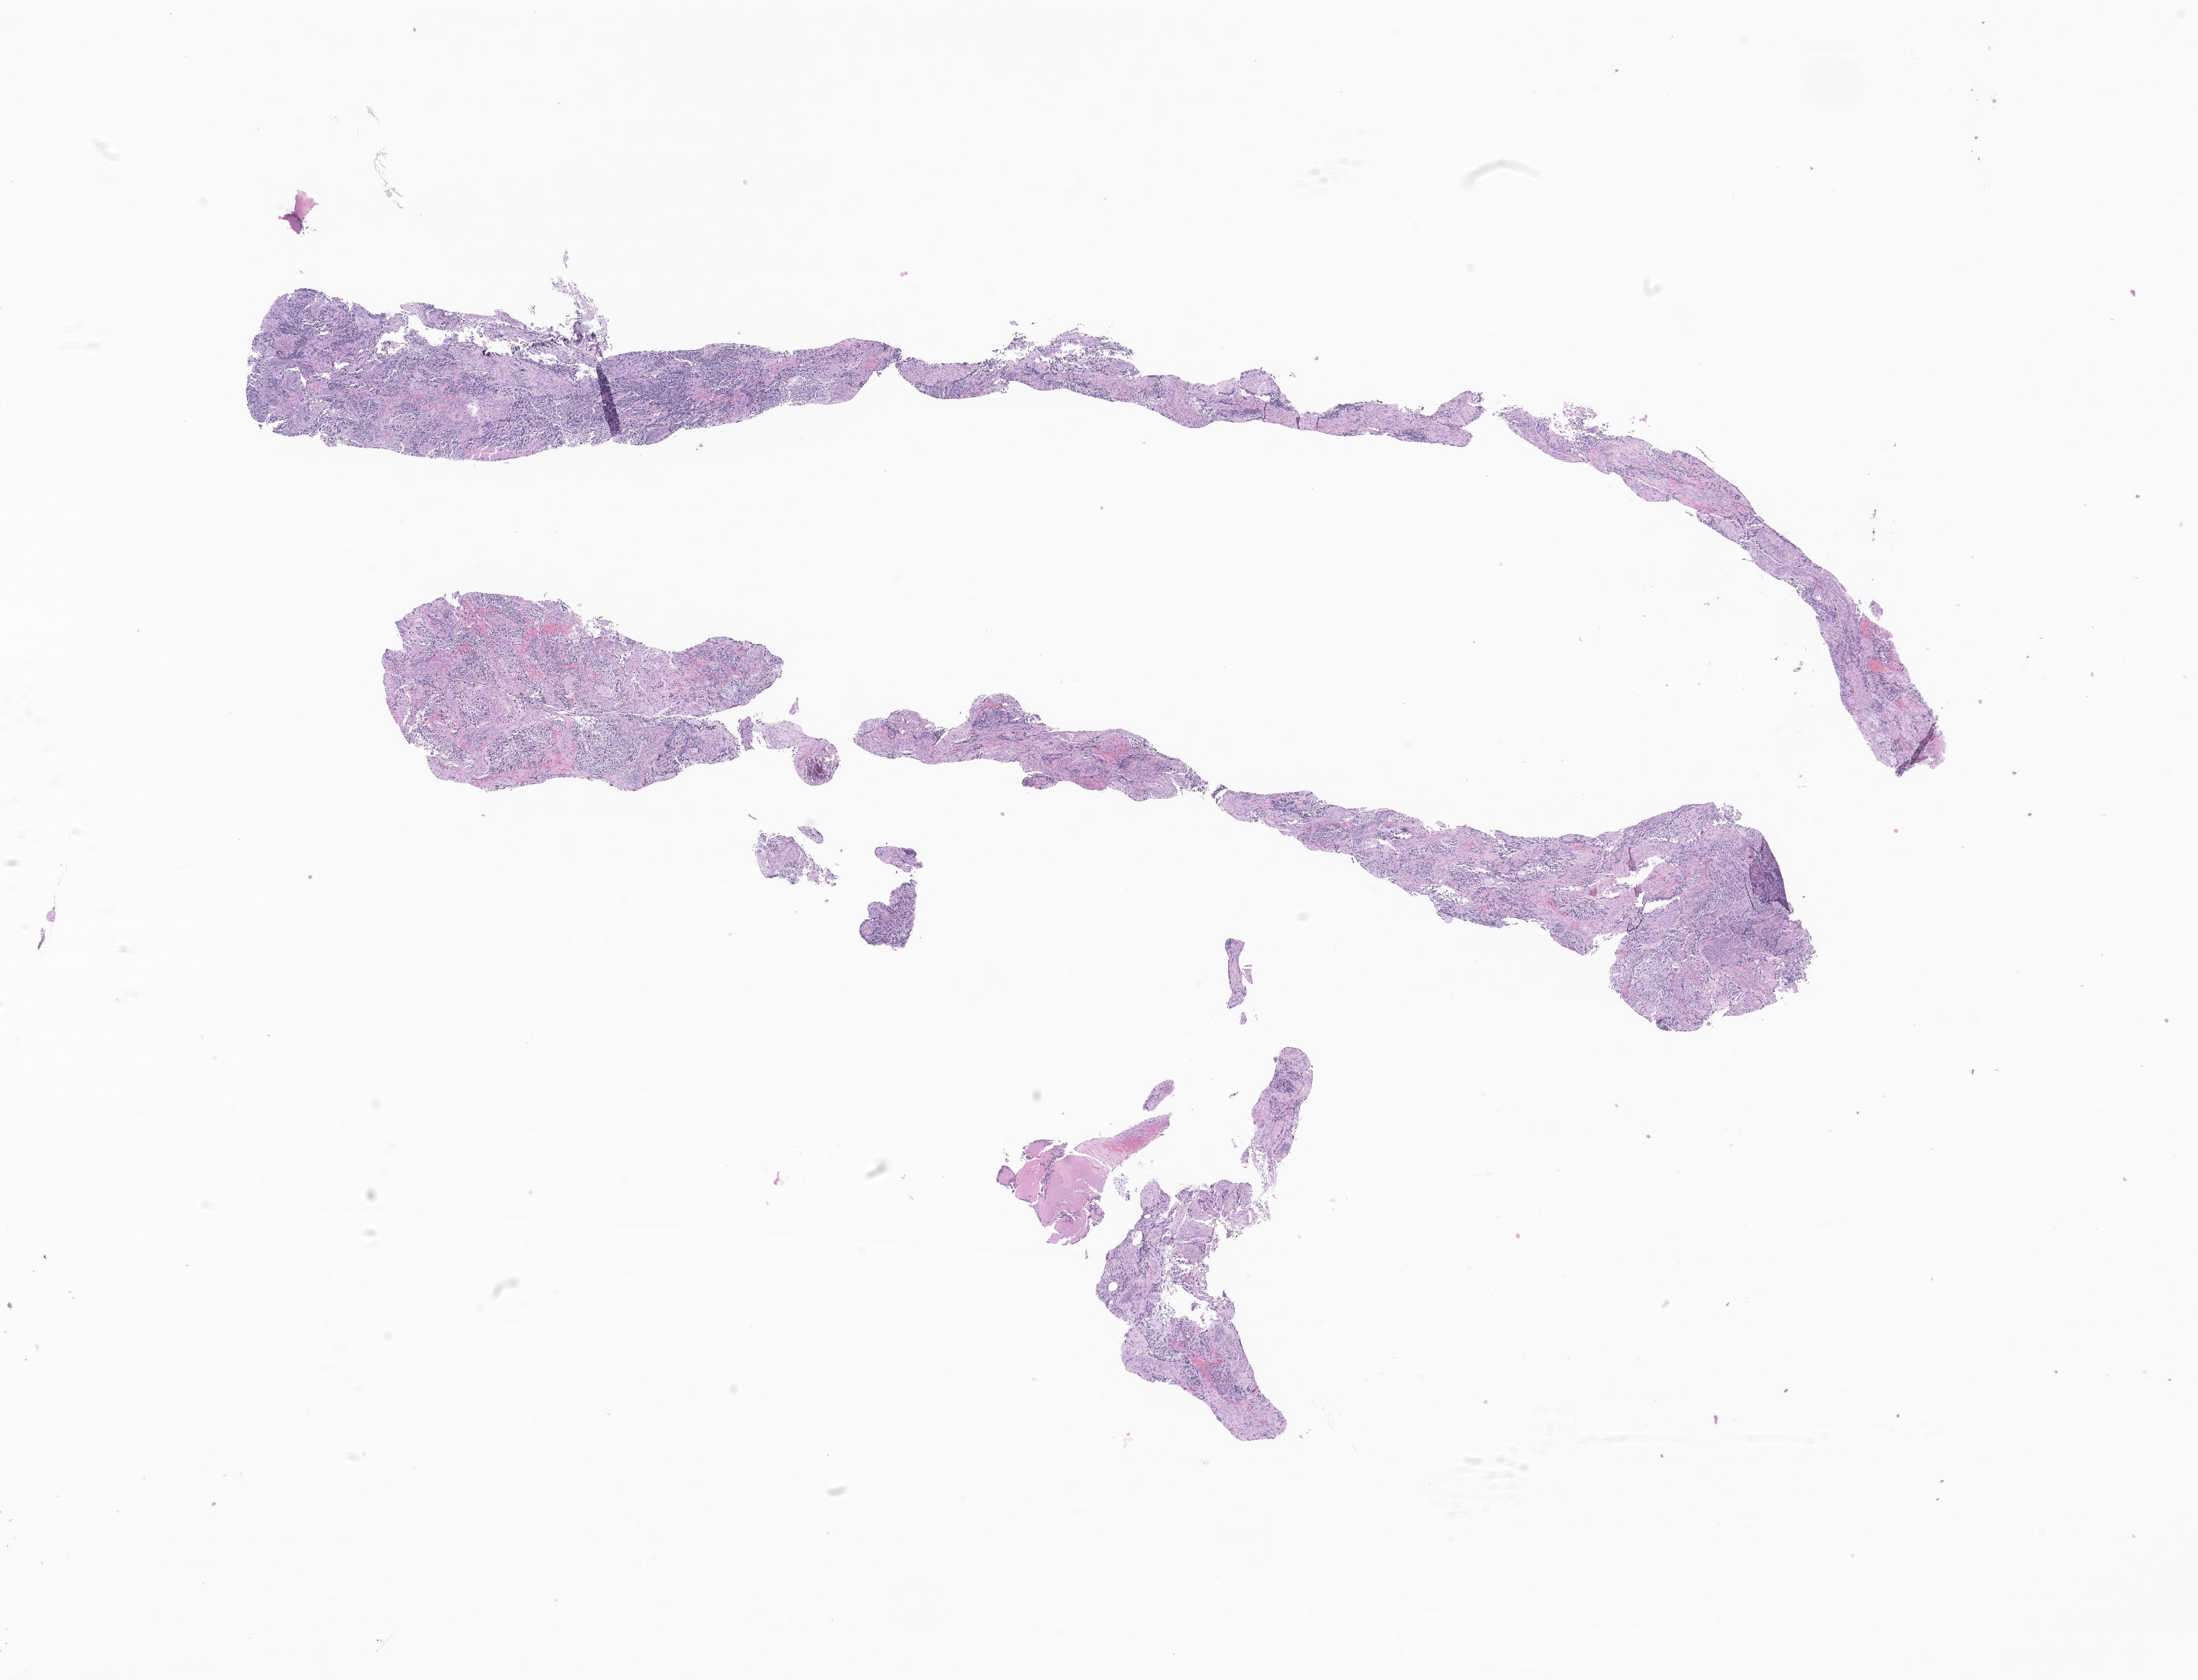
Digitized hematoxylin and eosin (H&E)-stained section of tumor tissue from the adrenal gland — shown as a low-resolution overview of the whole scanned area (about 17.3 x 13.2 mm); formalin-fixed paraffin-embedded section. Patient female; age 323 days.
- recorded diagnosis: Neuroblastoma, NOS